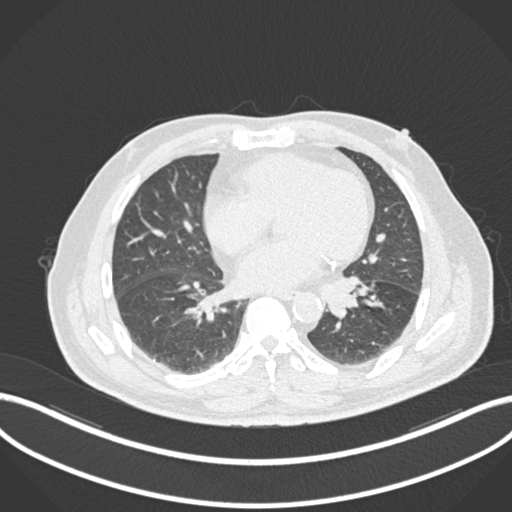
Chest CT, one axial slice. Position 49 of 161 along the scan axis. Reconstruction kernel B30f. Lung window (W 1500 / L -600 HU). 1 mm slice thickness. 512 × 512 image matrix, field of view 400 × 400 mm. Patient: male, 71 years. From the clinical record (not read from this slice): clinical TNM (as recorded): T1b N0 M0.
Structures marked on this image (rectangle marked by the reading radiologist):
- lung tumour (recorded histology: squamous cell carcinoma): bounding box [x1, y1, x2, y2] px = [326, 272, 364, 319]